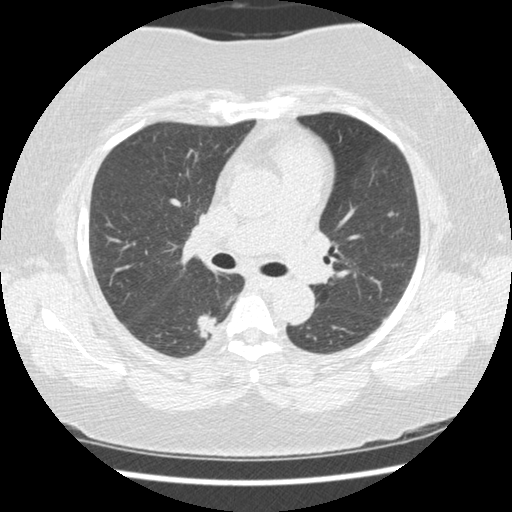
Axial slice from a low-dose chest CT screening exam; second screening round (one year after baseline); lung window (W 1500 / L -600 HU); 1.25 mm slice thickness; 120 kVp; 512 × 512 image matrix. Female, age 58 years at enrolment.
Expert reader's lesion annotation, bounding box <189,309,229,352> (left, top, right, bottom; pixels). Screening reader's record for this exam (one nodule recorded; not confirmed to be the boxed lesion): non-calcified nodule or mass ≥4 mm, right lower lobe, 15 × 15 mm, spiculated (stellate) margins, soft tissue attenuation, pre-existing on the prior screen: yes; interval growth: yes. Lung cancer was diagnosed 21 days after this screen: adenocarcinoma, NOS, right lower lobe, stage IB (AJCC 6th edition), 15 mm at pathology.